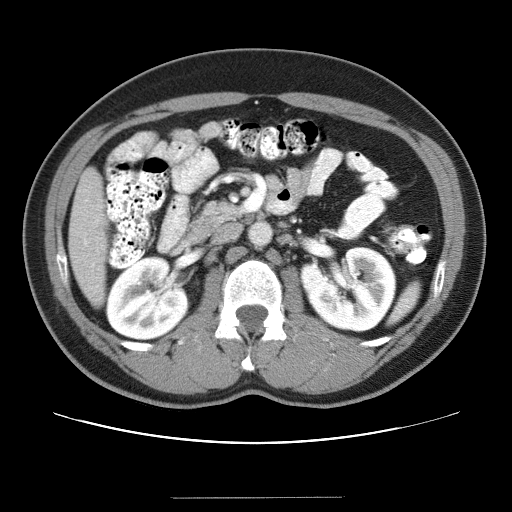
Contrast-enhanced abdominal CT (liver protocol), one axial slice. Position 8 of 40 along the scan axis. 120 kVp. Soft-tissue window (W 400 / L 40 HU). 512 × 512 image matrix, field of view 380 × 380 mm. Case-level facts recorded for this patient, not image findings: diagnosis: hepatocellular carcinoma (patient treated with transarterial chemoembolisation; whether this scan precedes or follows treatment is not stated here); TNM stage (as recorded): Stage-IVA; Child-Pugh class: B; tumour nodularity: multinodular.
Annotated regions visible in this slice (semi-automatically segmented with operator editing):
- liver parenchyma outside the tumour (the mass and vessels are separate outlines, so this box may not span the whole liver): bounding box (x1, y1, x2, y2) in pixels: (68, 168, 106, 304)
- liver vessels: (84, 219, 99, 265)